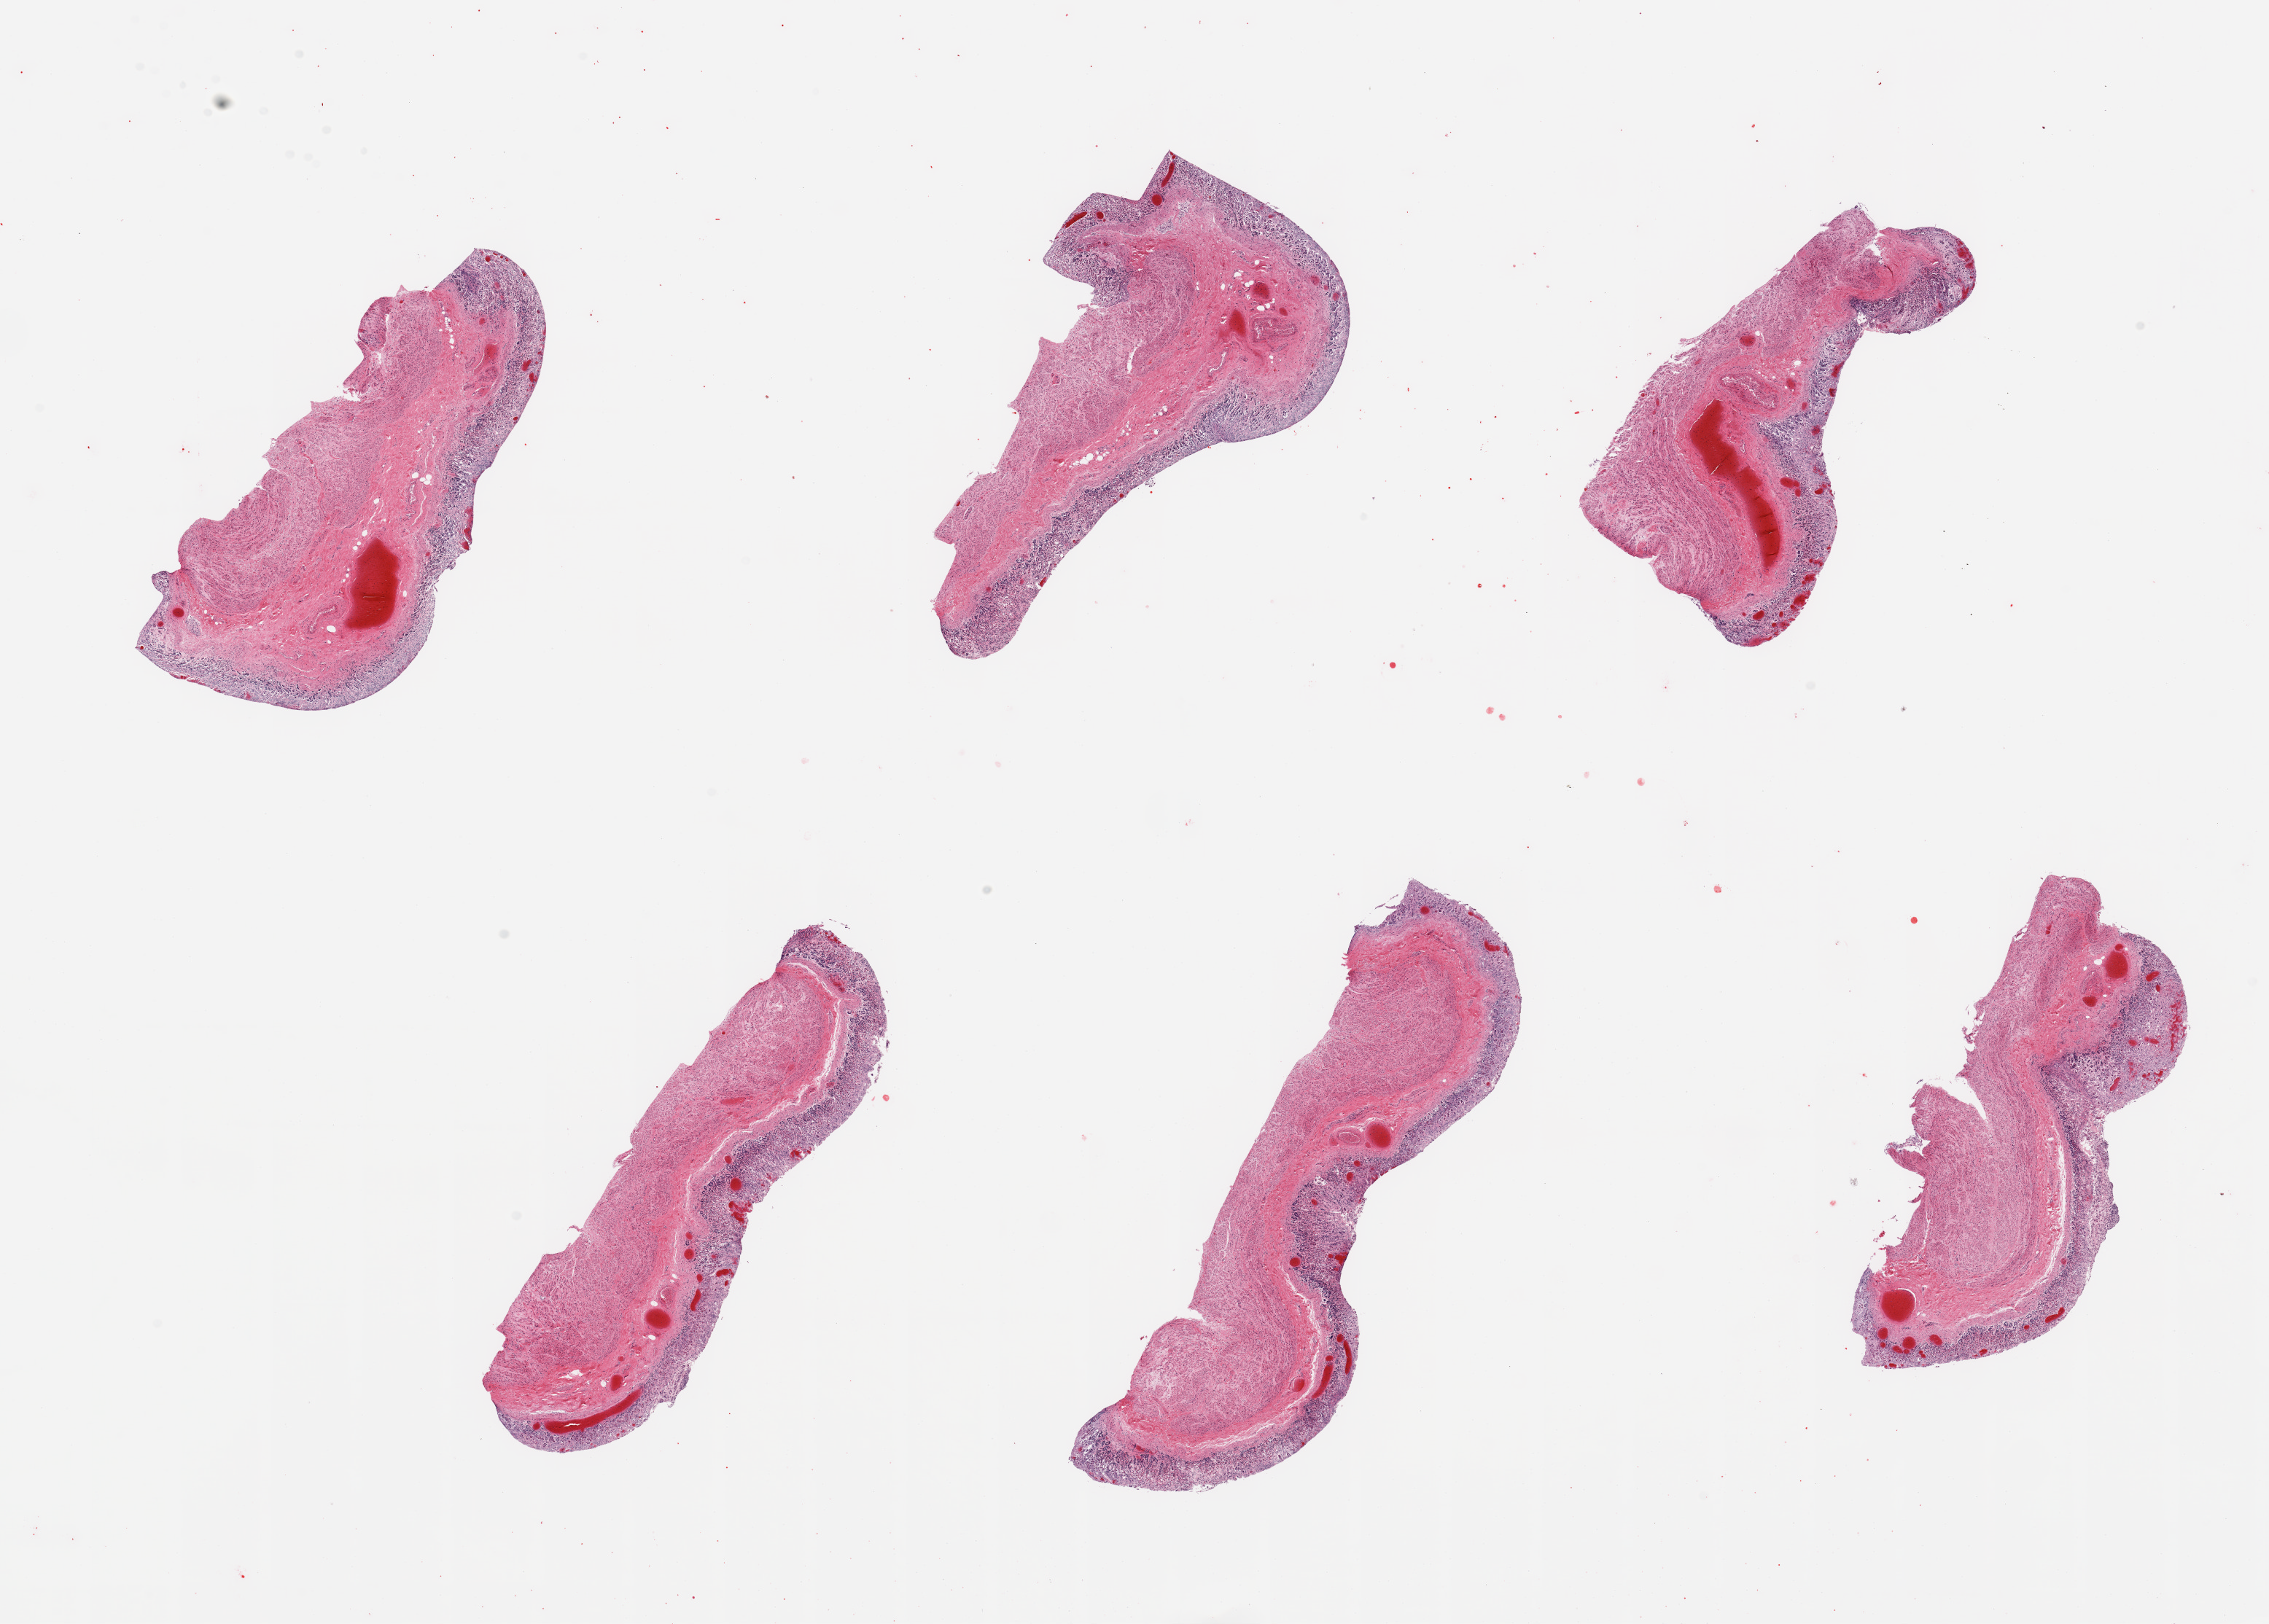
Whole-slide image, haematoxylin and eosin stain, shown as a low-resolution overview of the whole scanned area (about 24.6 x 17.6 mm). PAXgene-fixed paraffin-embedded (PFPE) section. Sampled site (target tissue): stomach. Tissue donor sample. Donor sex: female.
• pathologist's review note for this sample: 6 pieces; mucosa largely autolyzed; muscularis moderately autolyzed